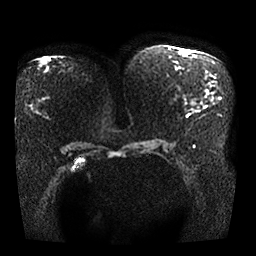
Breast MRI, one axial slice. Slice 8 of 25 in the series (ordered by position). Diffusion-weighted series; image 2 of 4 stored at this slice position (different b-values; order by instance number). 1.5 T. 4 mm slice thickness. 256 × 256 image matrix. Female patient.
Structures marked on this image (expert manual segmentation):
- tumour on diffusion-weighted imaging: bounding box [x1, y1, x2, y2] px = [194, 105, 201, 111]